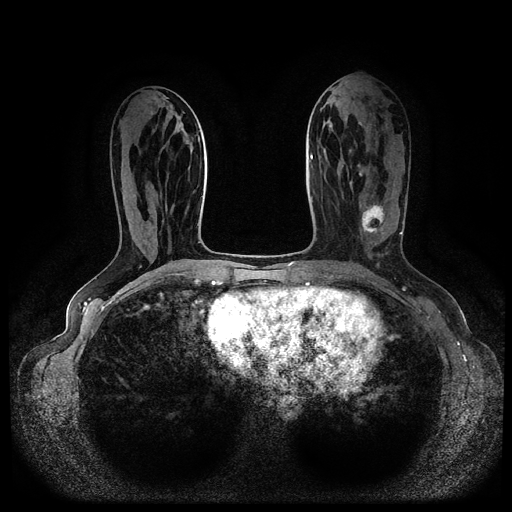
Breast MRI (dynamic contrast-enhanced, multi-phase), one axial slice; slice 42 of 116 in the series (ordered by position); dynamic contrast-enhanced series, time point 2 of 5 at this slice position (early post-contrast); 1.5 T; TE 2.6 ms, TR 5.3 ms; 2 mm slice thickness; 512 × 512 image matrix, field of view 350 × 350 mm. Female patient, age 45 years.
Structures marked on this image (semi-automatically segmented with operator editing):
- breast lesion (labelled 'tumour' in the annotation; benign lesions carry a separate 'benign' label): bounding box (x1, y1, x2, y2) in pixels: (357, 203, 389, 240)